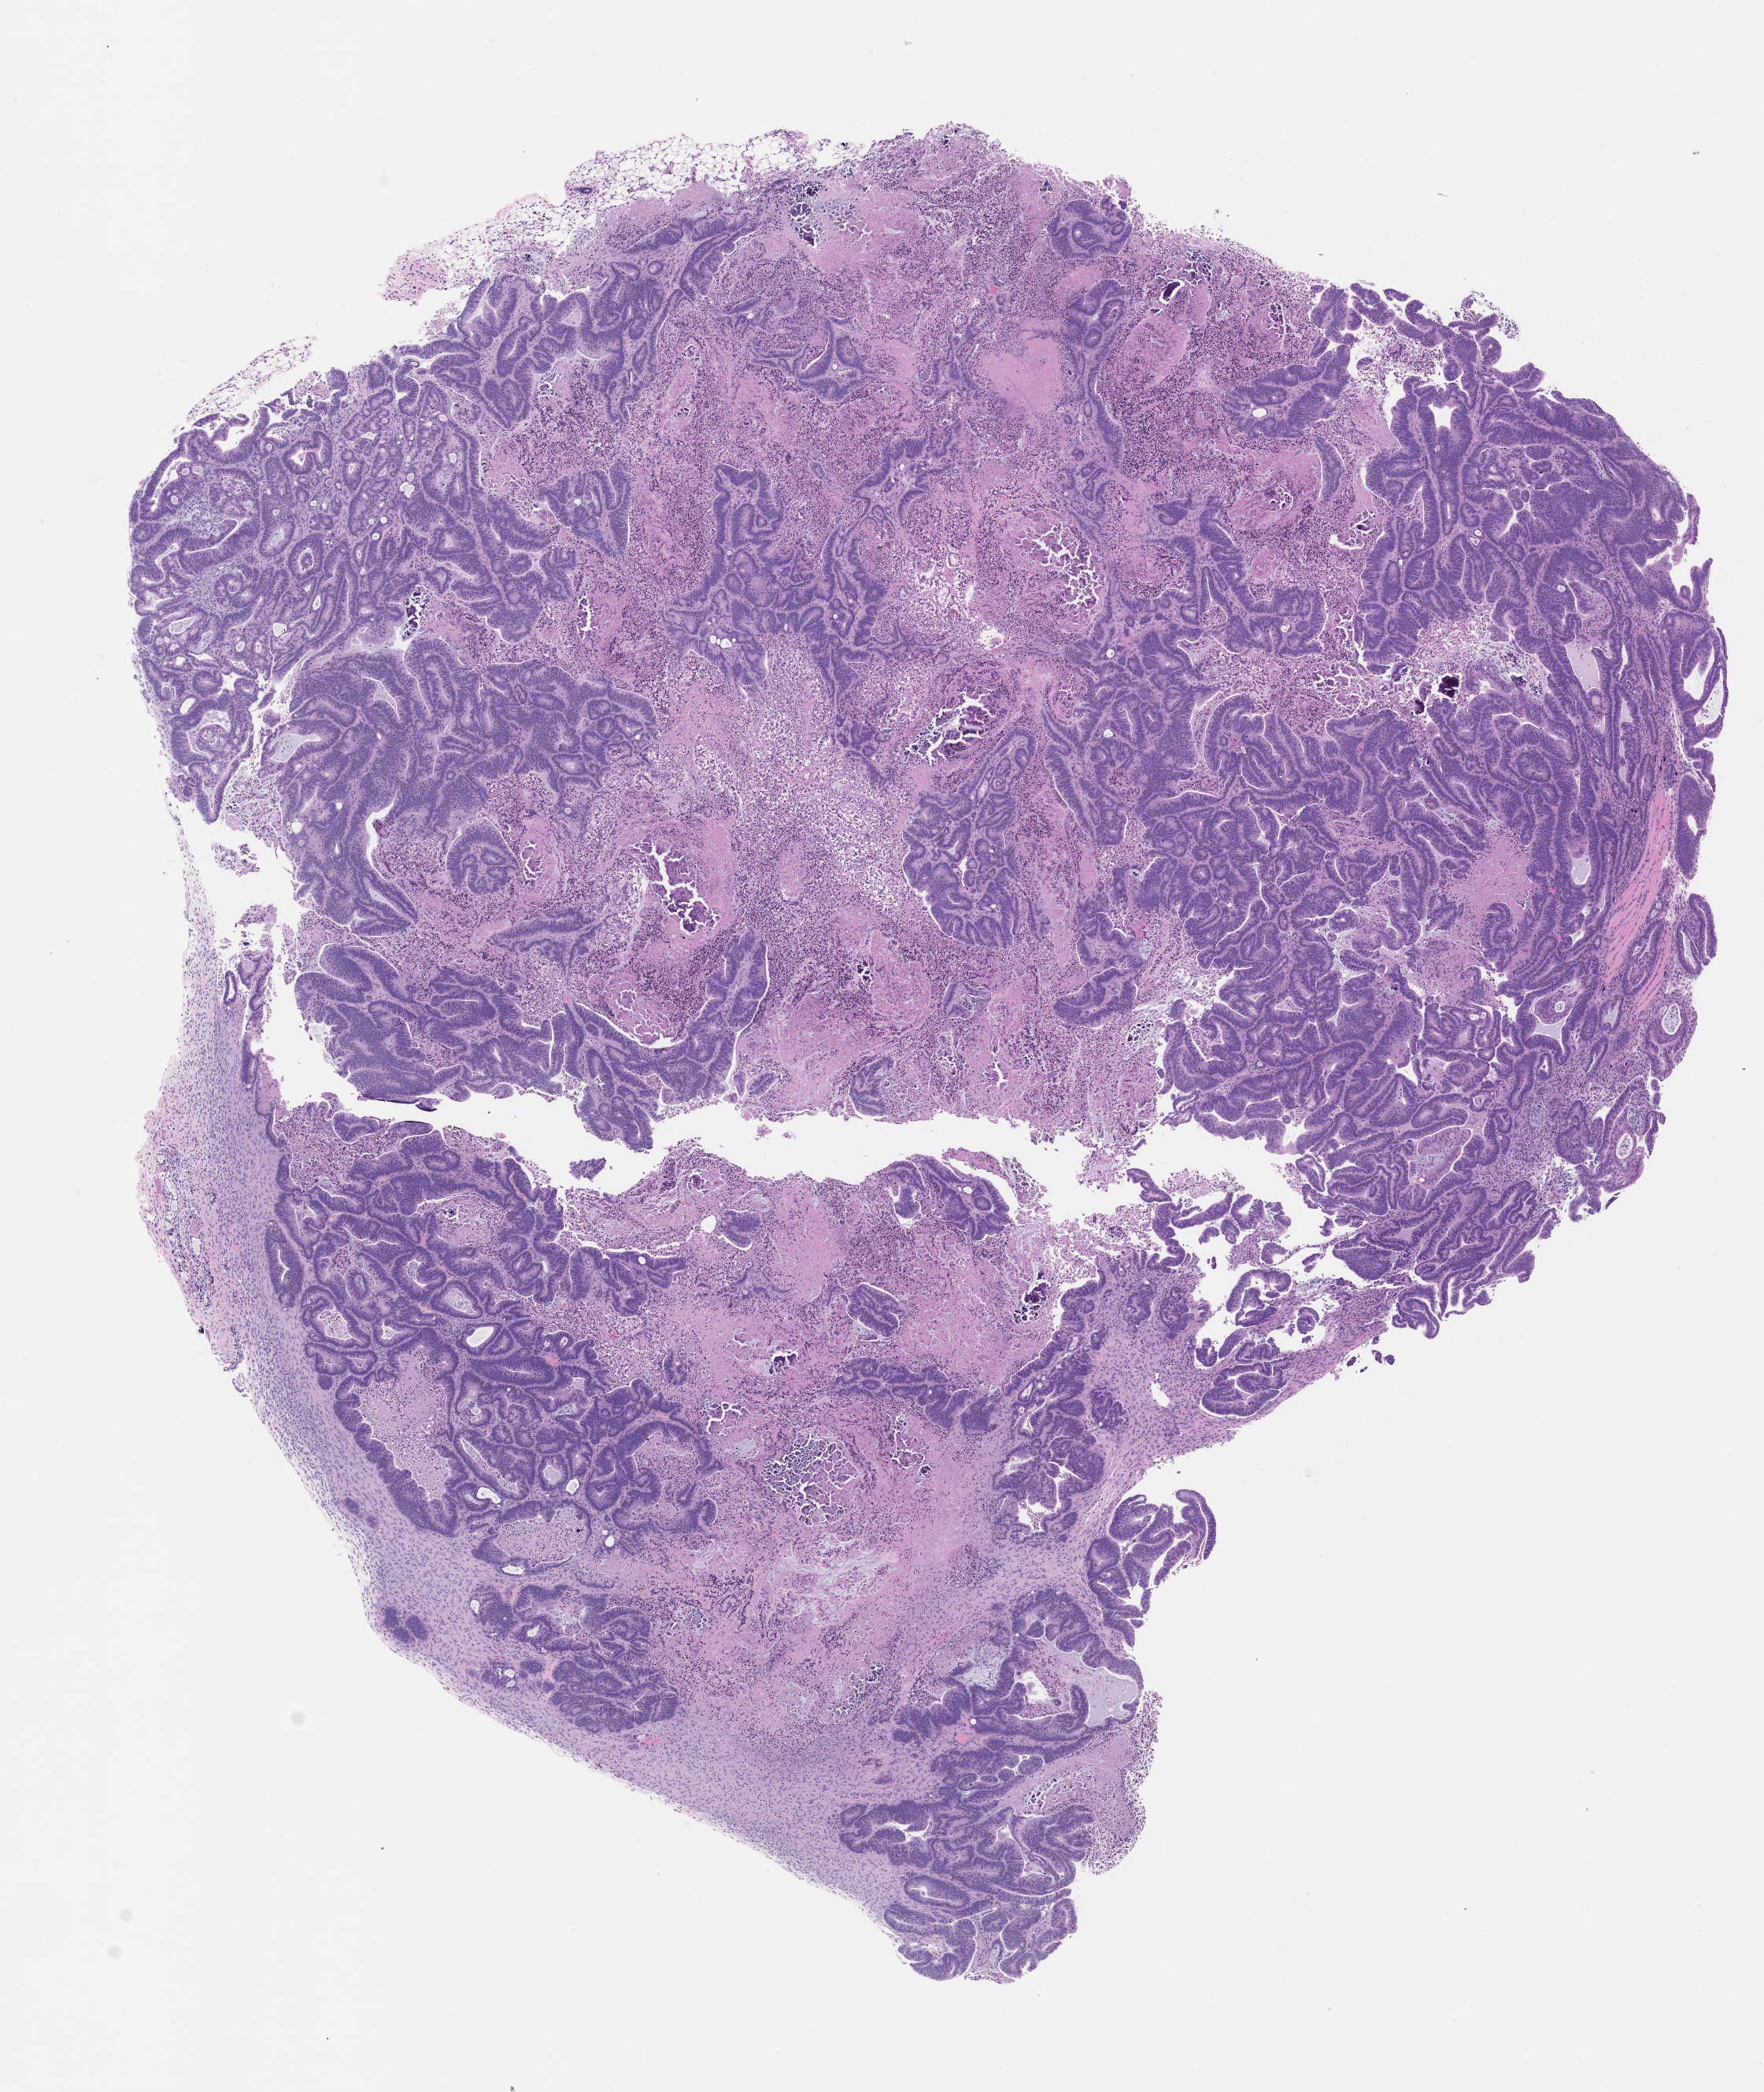
Whole-slide image, H&E: patient-derived xenograft (human tumor grown in a mouse), passage 3 — a low-resolution overview of the entire scanned area, about 9.0 x 10.7 mm, FFPE section, originating tumor site category: colon.
Originating patient diagnosis: Colon Adenocarcinoma.